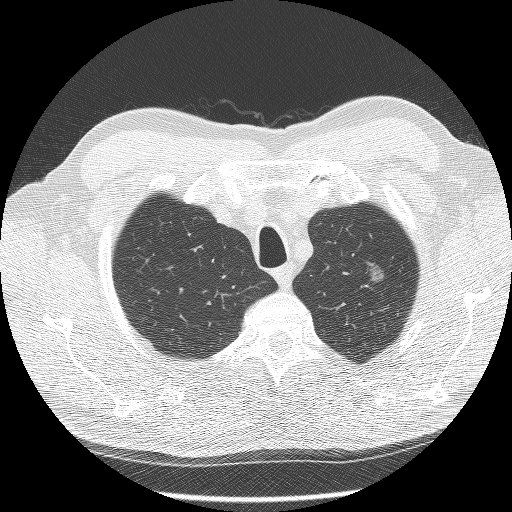
Axial slice from a low-dose chest CT screening exam, second annual screen, lung window (W 1500 / L -600 HU), lung (sharp) reconstruction kernel (BONE), 512 × 512 image matrix. Male, age 60 years at enrolment.
Expert-annotated lung lesion, bounding box <347,256,400,299> (left, top, right, bottom; pixels). The screening reader recorded 2 non-calcified nodules or masses ≥4 mm on this exam (right lower lobe, left upper lobe); which of them this box marks is not recorded. Official screen result: positive, no significant change: stable abnormalities potentially related to lung cancer, unchanged since the prior screening exam. Lung cancer was diagnosed 448 days after this screen: bronchiolo-alveolar carcinoma, non-mucinous, left upper lobe, well differentiated (G1), stage IA (AJCC 6th edition), 16 mm at pathology.